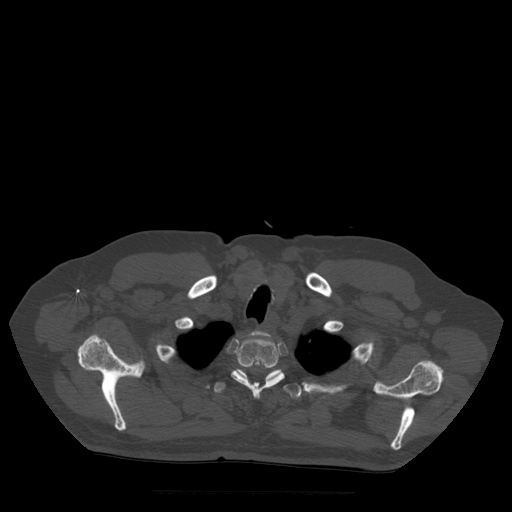
CT including the spine, one axial slice; bone window (W 1800 / L 400 HU); 1.25 mm slice thickness; 512 × 512 image matrix, field of view 420 × 420 mm. Patient age 72 years. From the clinical record (not read from this slice): primary cancer: prostate.
Structures marked on this image (semi-automatic segmentation, software-assisted and operator-edited):
- T1 vertebra: bounding box [x1, y1, x2, y2] px = [252, 331, 270, 337]
- T2 vertebra: [232, 334, 285, 398]
- T3 vertebra: [214, 367, 302, 399]